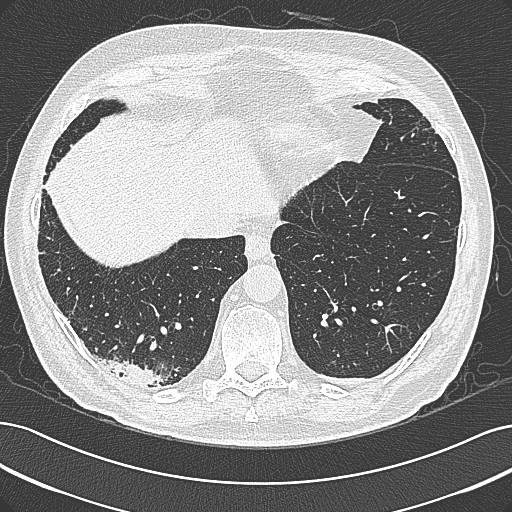
Chest CT (low-dose screening protocol), one axial image; first (baseline) screen; lung window (W 1500 / L -600 HU); slice 229 of 355 in the series. Male participant, aged 68 years at enrolment. Former smoker at enrolment.
Lesion marked by an expert reader, bounding box (x1, y1, x2, y2) in pixels: (97, 341, 183, 402). No non-calcified nodule or mass ≥4 mm was recorded by the screening reader at this exam. Official screen result: negative screen, significant abnormalities not suspicious for lung cancer. Lung cancer was diagnosed 154 days after this screen: mucinous adenocarcinoma, right lower lobe, well differentiated (G1), stage IB (AJCC 6th edition), 50 mm at pathology.